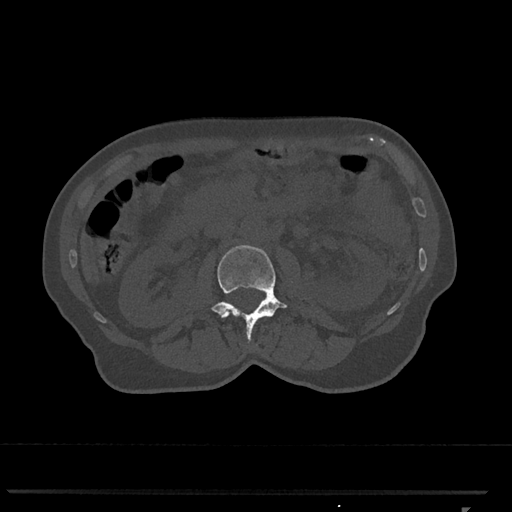
CT including the spine, one axial slice. Position 337 of 793 along the scan axis. Reconstruction kernel Br40s/3. 120 kVp. Bone window (W 1800 / L 400 HU). 0.5 mm slice thickness. 512 × 512 image matrix. Patient: female, 62 years. Case-level facts recorded for this patient, not image findings: primary cancer: renal.
Annotated regions visible in this slice (semi-automatically segmented with operator editing):
- L2 vertebra: bounding box (x1, y1, x2, y2) in pixels: (211, 245, 288, 341)